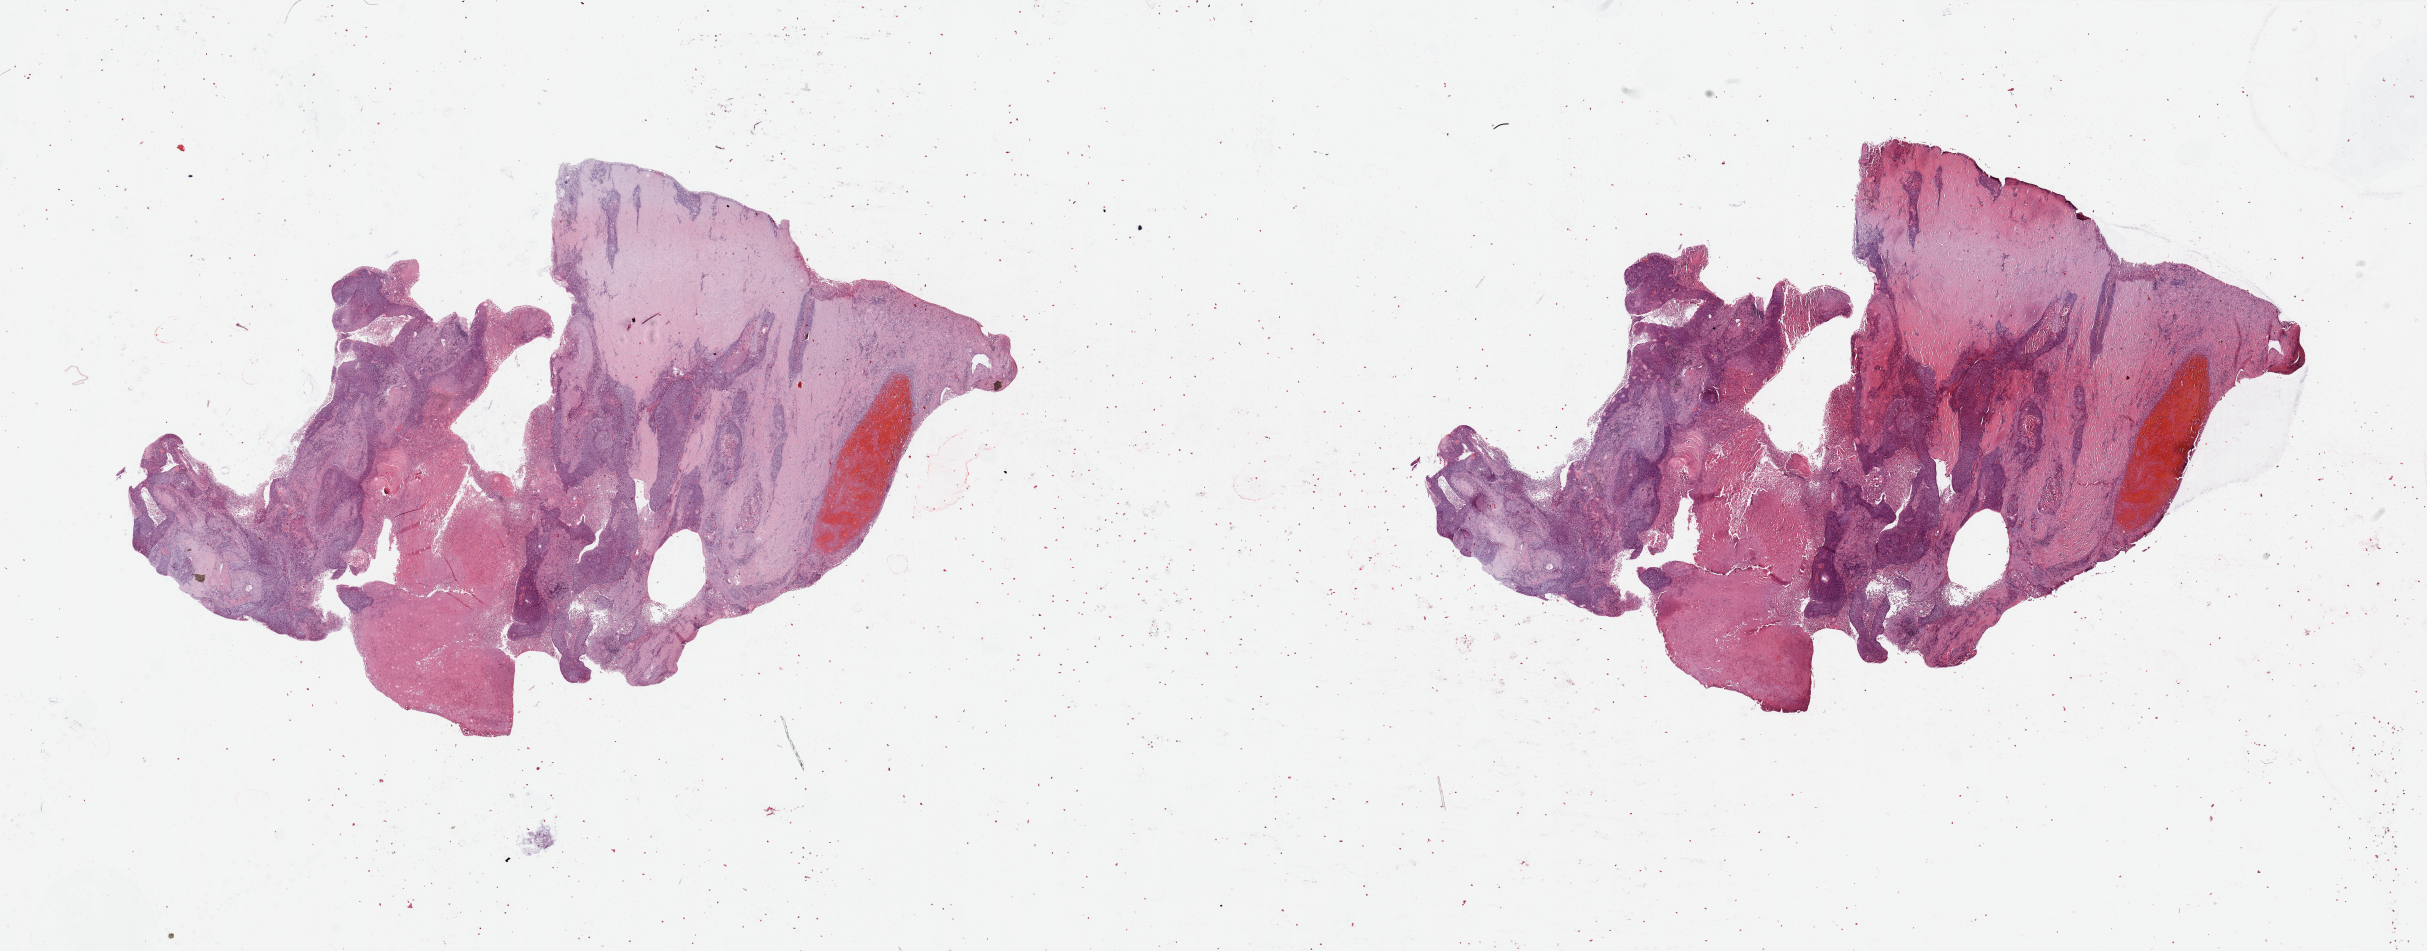
H&E whole-slide image — a low-resolution overview of the entire scanned area, about 38.4 x 15.0 mm, lung, tumour tissue. Male, 70 y/o. Histologic grade: G3 (poorly differentiated).
Diagnosis: Squamous cell carcinoma, NOS. AJCC pathologic stage: IIIA. Primary tumour site (as recorded): right lower lobe.